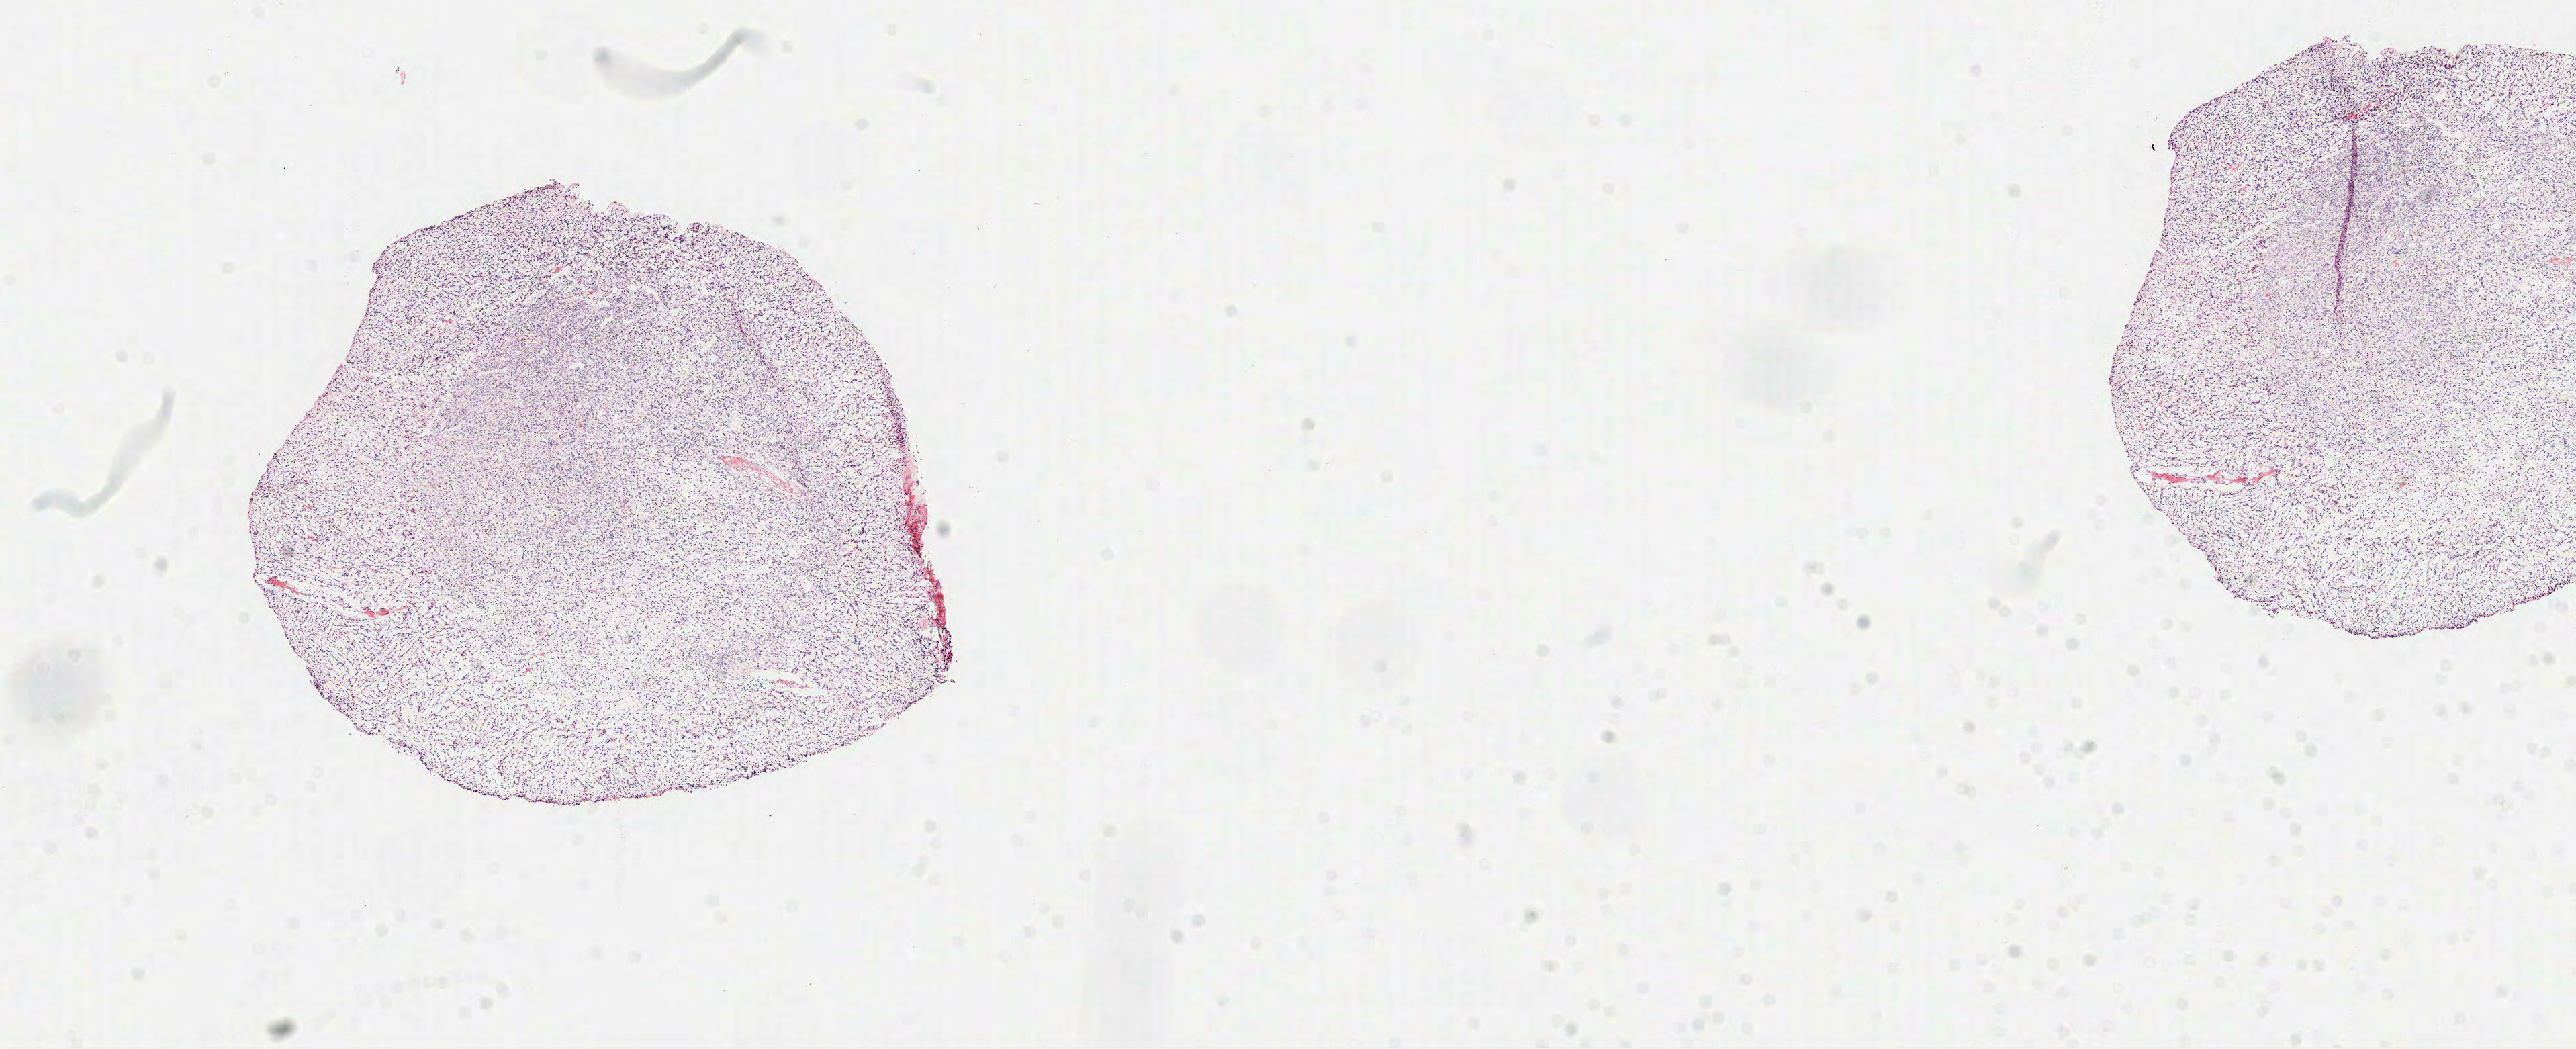
Digitized H&E tissue section (whole slide) — shown as a low-resolution overview of the whole scanned area (about 15.5 x 6.3 mm). Formalin-fixed paraffin-embedded (FFPE) diagnostic section. Brain, primary tumour sample. Female, age 69 years at initial diagnosis.
• diagnosis: Glioblastoma